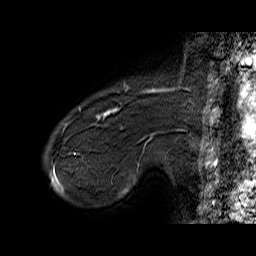
Breast MRI (dynamic contrast-enhanced), one sagittal slice. Slice 9 of 60 in the series (ordered by position). Dynamic contrast-enhanced series, time point 2 of 6 at this slice position (early post-contrast). 1.5 T. TE 6.4 ms, TR 32.9 ms. 4 mm slice thickness. 256 × 256 image matrix. Female patient. Case-level facts recorded for this patient, not image findings: setting: breast cancer imaged before/during neoadjuvant chemotherapy; receptor status: HER2-positive.
Annotated regions visible in this slice (semi-automatically segmented with operator editing):
- analysis volume of interest (the breast-tissue region the enhancement analysis was run in; not a lesion): bounding box [x1, y1, x2, y2] px = [71, 80, 155, 146]
- tumour enhancement mask (voxels above the 100 % enhancement threshold inside the analysis volume of interest): [97, 87, 155, 140]